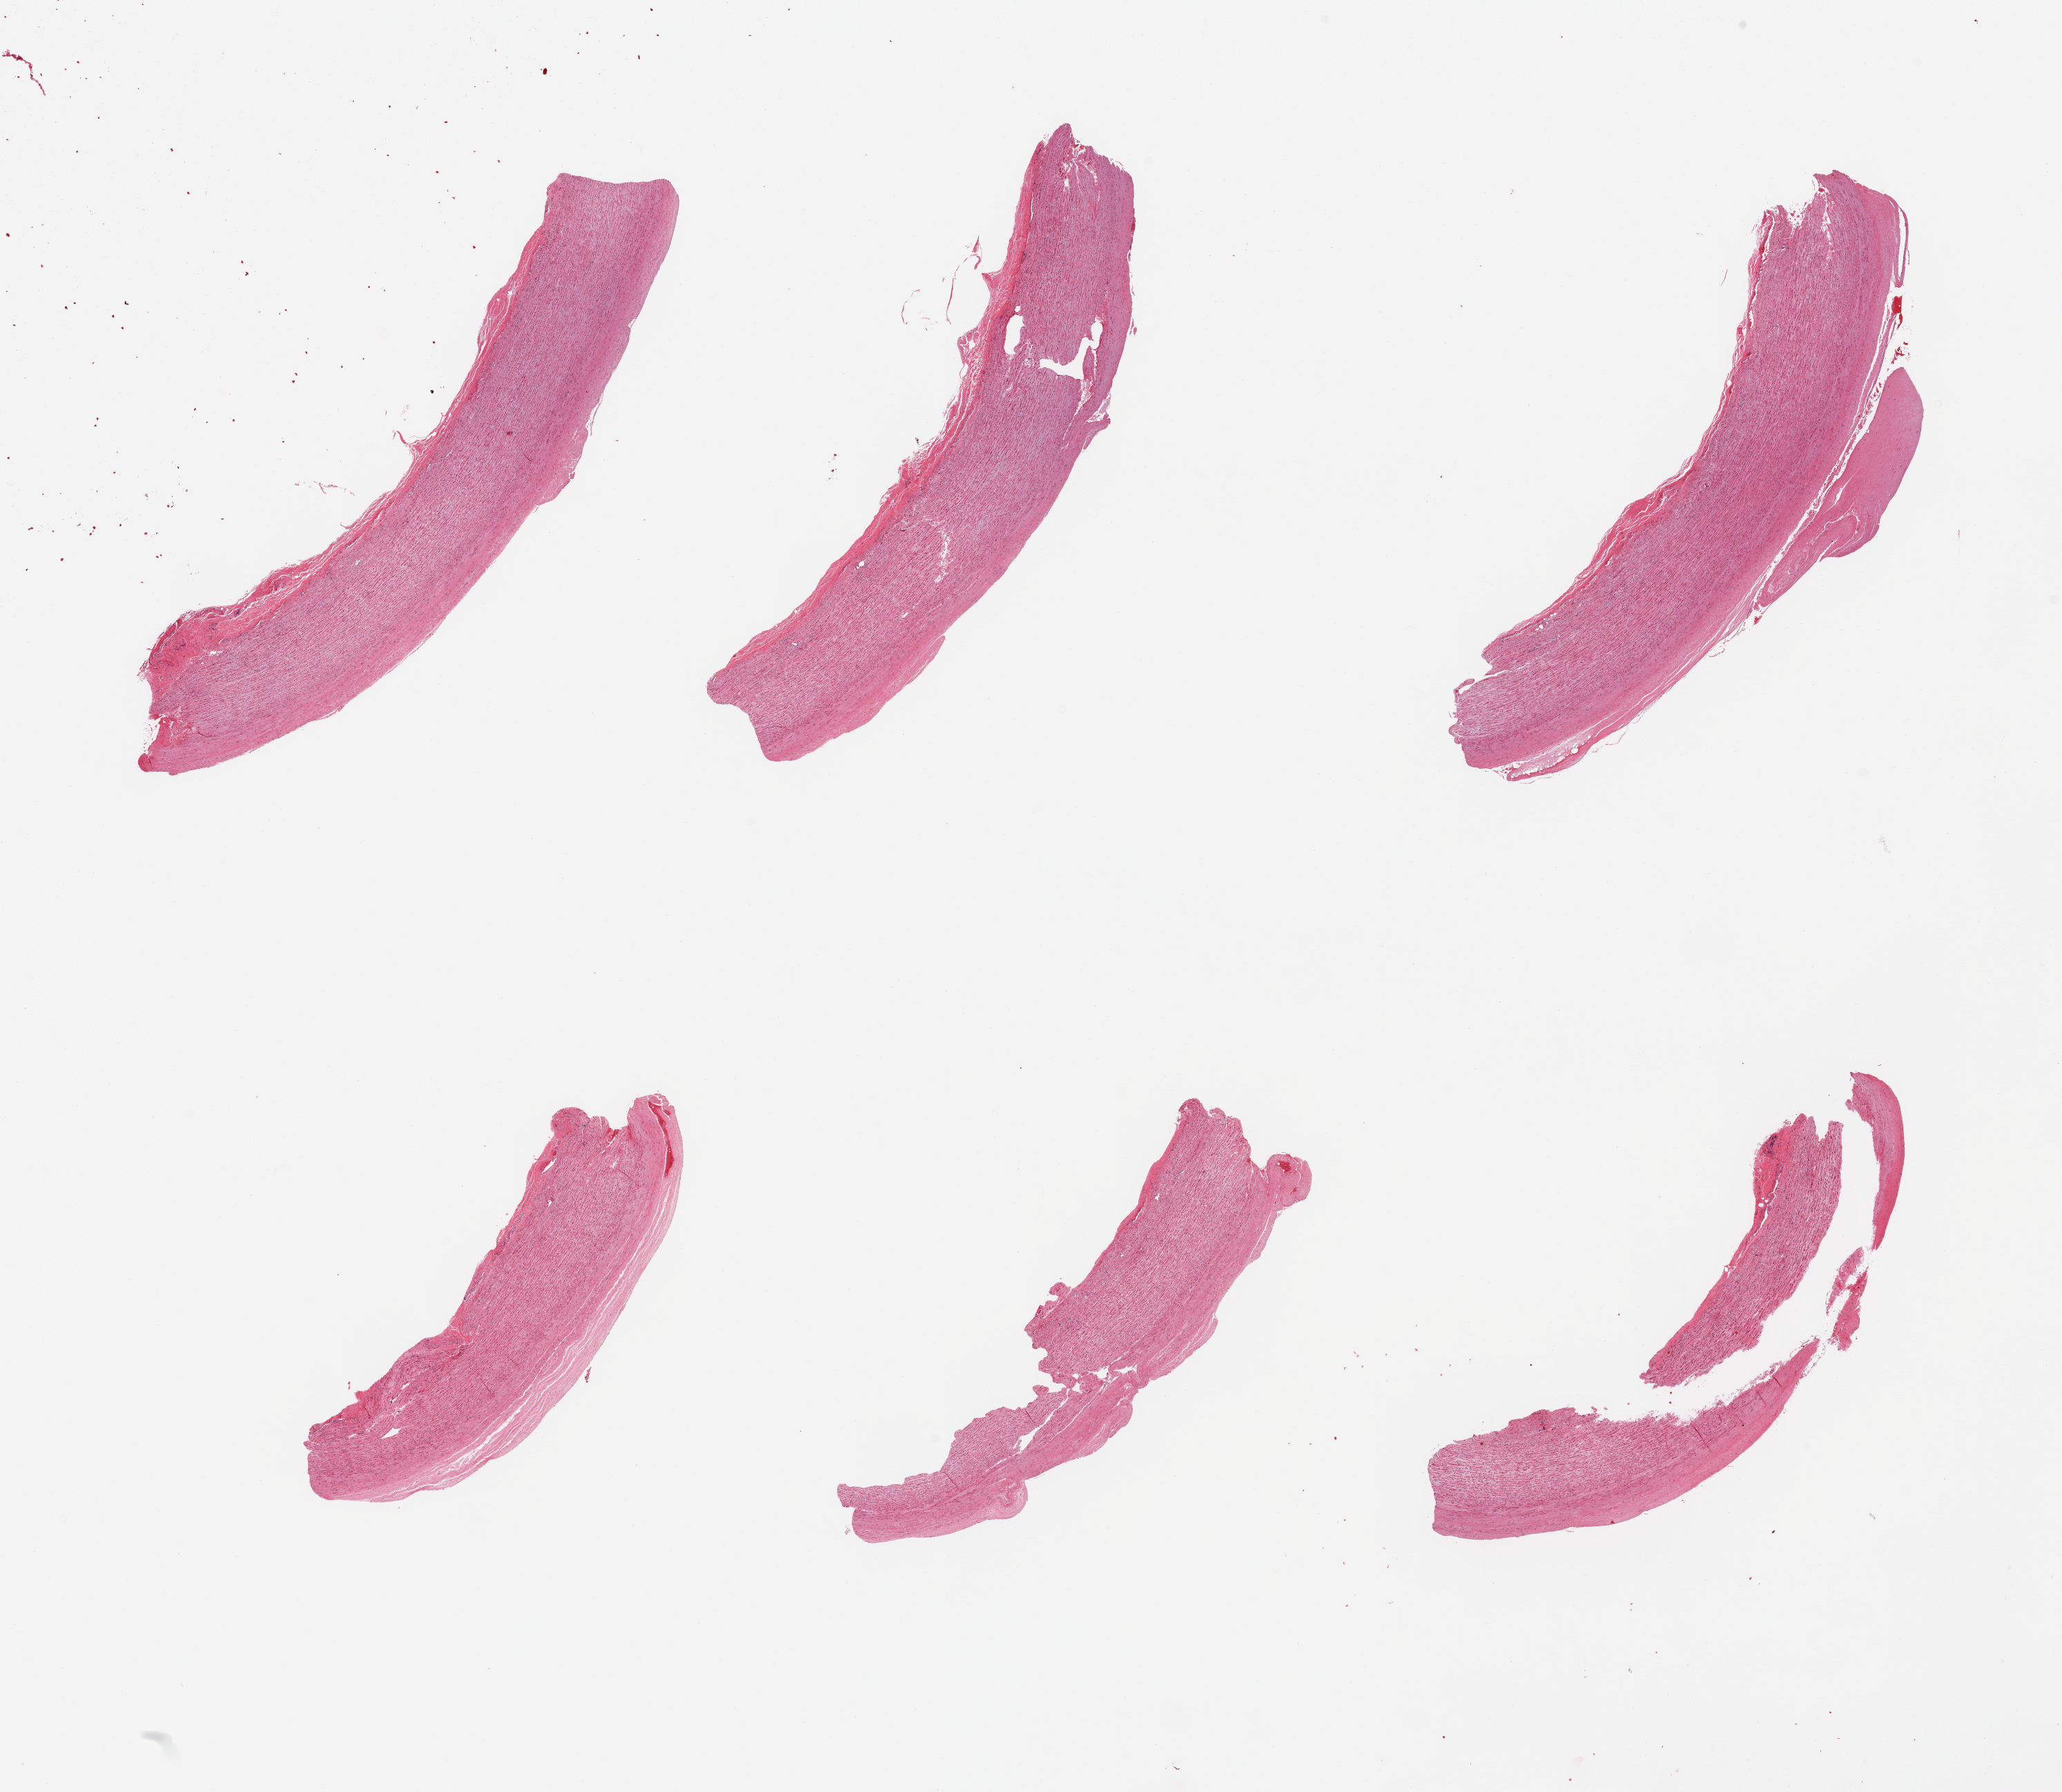
Hematoxylin and eosin (H&E) whole-slide image, shown as a low-resolution overview of the whole scanned area (about 23.6 x 20.5 mm, from a 20x scan); PAXgene-fixed paraffin-embedded (PFPE) section; sampled site (target tissue): aorta; donor tissue sample. Male donor.
Pathologist's review note for this sample: 6 pieces; thin flat intimal plaques.